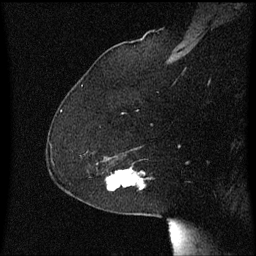
Breast MRI (dynamic contrast-enhanced), one sagittal slice; position 43 of 60 along the scan axis; dynamic contrast-enhanced series, image 2 of 3 at this slice position (ordered by acquisition); 1.5 T; TE 4.2 ms, TR 8.4 ms; 2 mm slice thickness; 256 × 256 image matrix, field of view 200 × 200 mm. Female patient, age 59 years.
Structures marked on this image (semi-automatically segmented with operator editing):
- analysis volume of interest (the breast-tissue region the enhancement analysis was run in; not a lesion): bounding box <106,166,145,191> (left, top, right, bottom; pixels)
- tumour enhancement mask (voxels above the 70 % enhancement threshold inside the analysis volume of interest): <134,180,143,183>